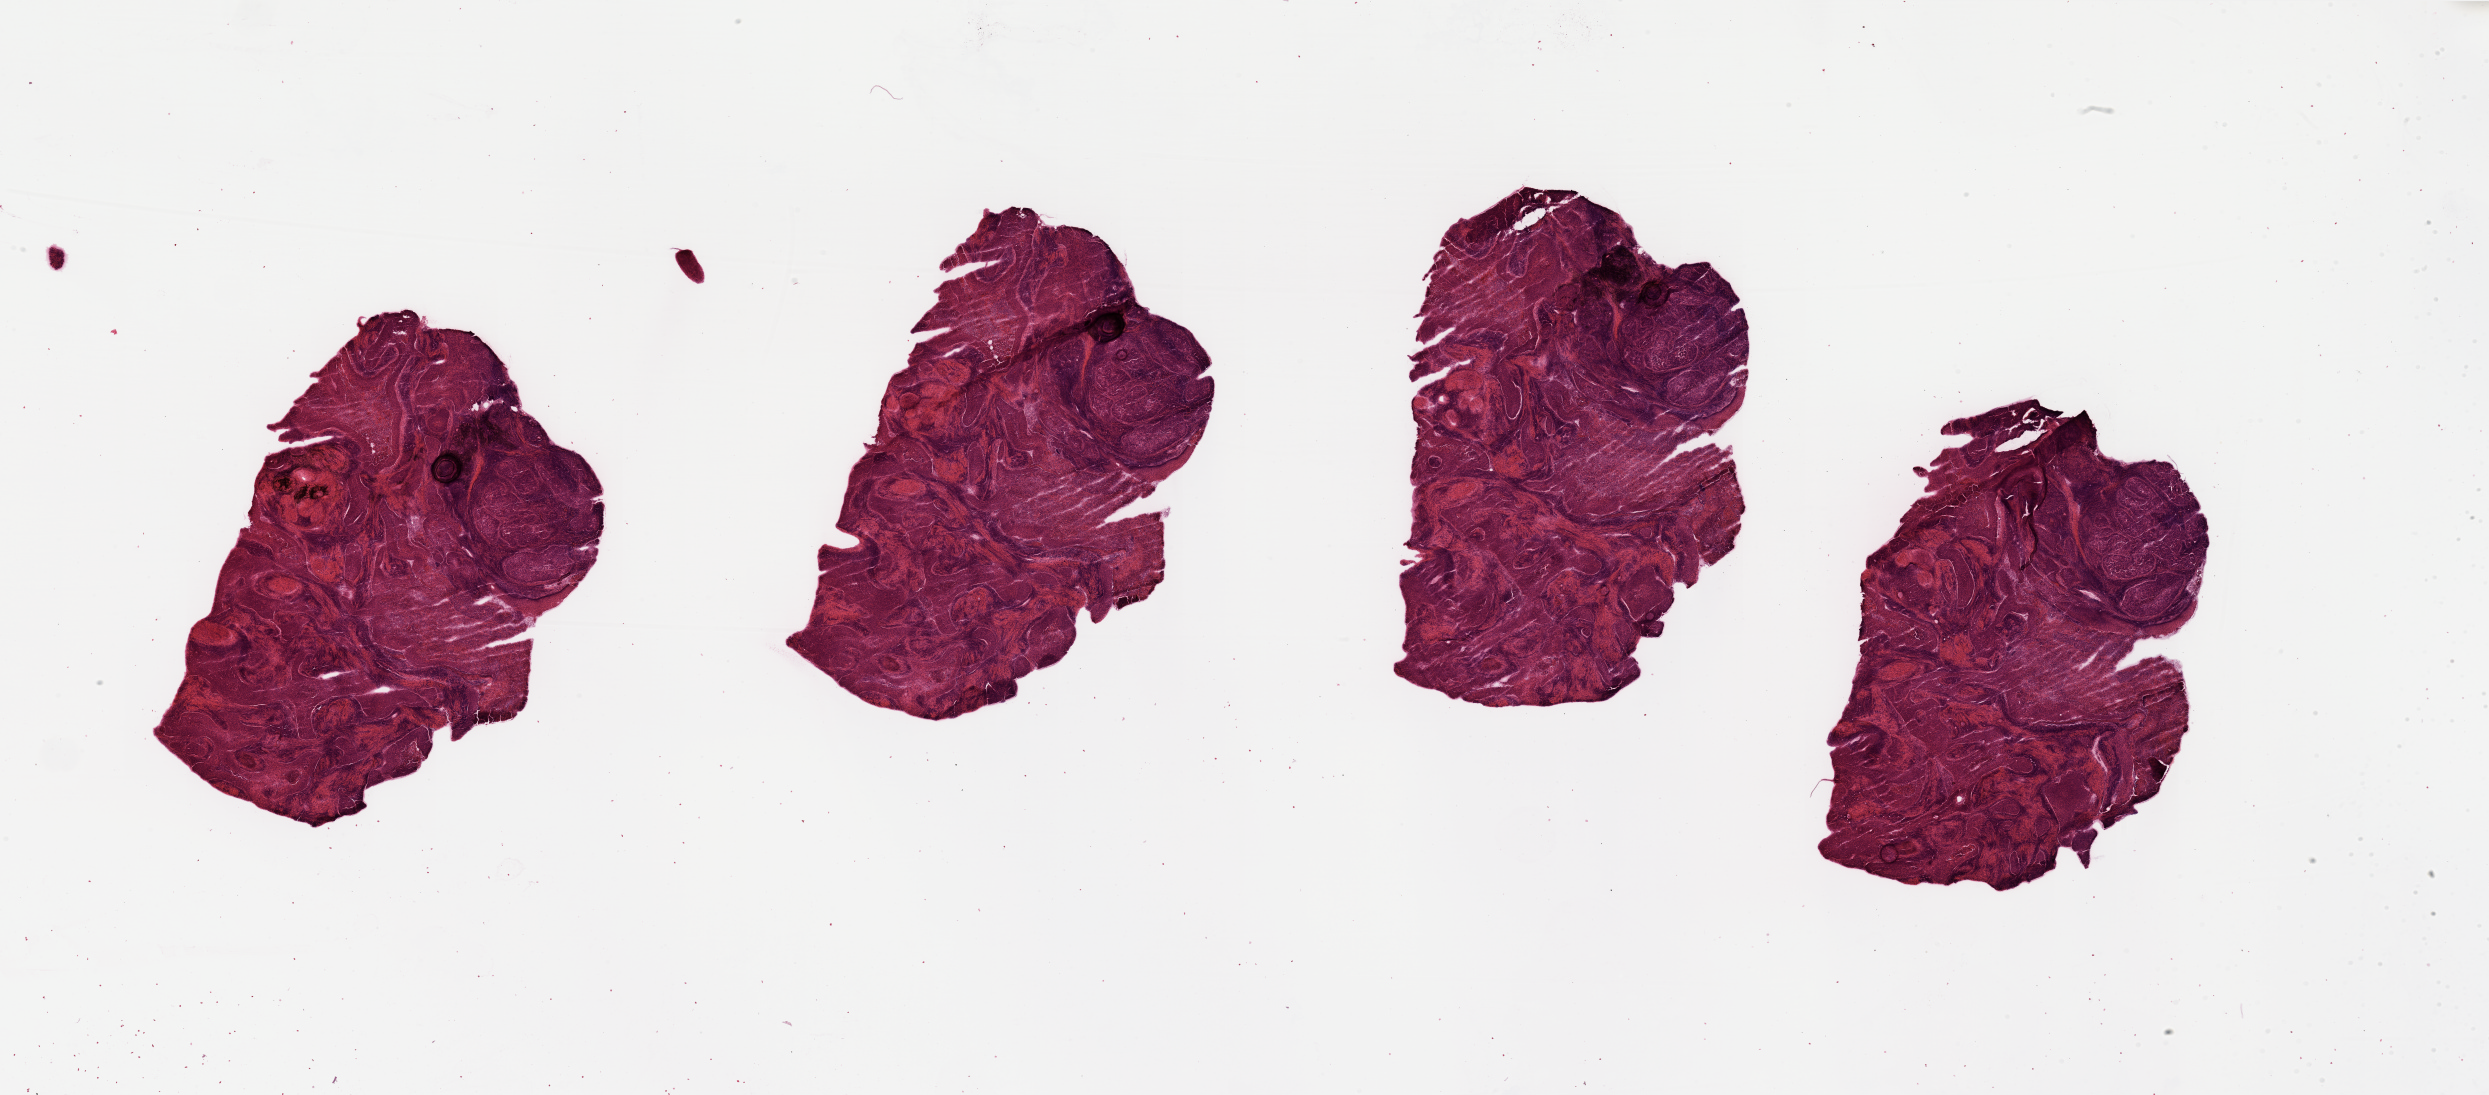
Whole-slide histology image, Hematoxylin and eosin (H&E) stained — whole scanned area (about 39.4 x 17.3 mm) shown as a low-resolution overview; head and neck, tissue type not recorded. Patient: male, age 67 years.
Patient diagnosis: Squamous cell carcinoma, NOS (larynx, NOS).